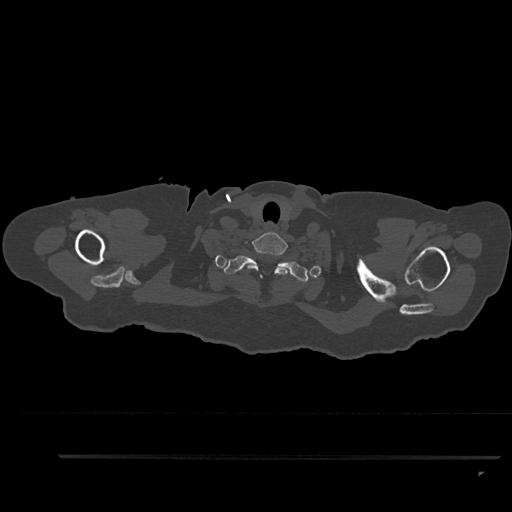
CT including the spine, one axial slice. Position 778 of 797 along the scan axis. Reconstruction kernel Br40s/3. Bone window (W 1800 / L 400 HU). 0.5 mm slice thickness. 512 × 512 image matrix. Female patient, age 44 years. Case-level facts recorded for this patient, not image findings: primary cancer: renal; vertebrae with lytic lesions (as recorded): L1.
Structures marked on this image (semi-automatically segmented with operator editing):
- T1 vertebra: box from (x=224, y=255) to (x=309, y=282) px